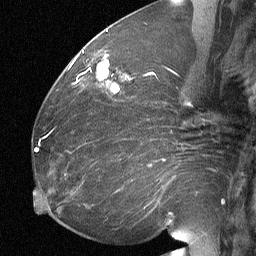
Breast MRI (dynamic contrast-enhanced), one sagittal slice; position 30 of 64 along the scan axis; dynamic contrast-enhanced study with each time point stored as its own series, time point 2 of 3 at this slice position (early post-contrast, ordered by acquisition time); 1.5 T; TE 4.8 ms, TR 27 ms; 256 × 256 image matrix, field of view 200 × 200 mm. Patient: female, 60 years. From the clinical record (not read from this slice): setting: breast cancer imaged before/during neoadjuvant chemotherapy; receptor status: HR-positive, HER2-negative.
Structures marked on this image (semi-automatic segmentation, software-assisted and operator-edited):
- analysis volume of interest (the breast-tissue region the enhancement analysis was run in; not a lesion): bounding box (x1, y1, x2, y2) in pixels: (91, 56, 124, 102)
- tumour enhancement mask (voxels above the 90 % enhancement threshold inside the analysis volume of interest): (97, 56, 118, 92)